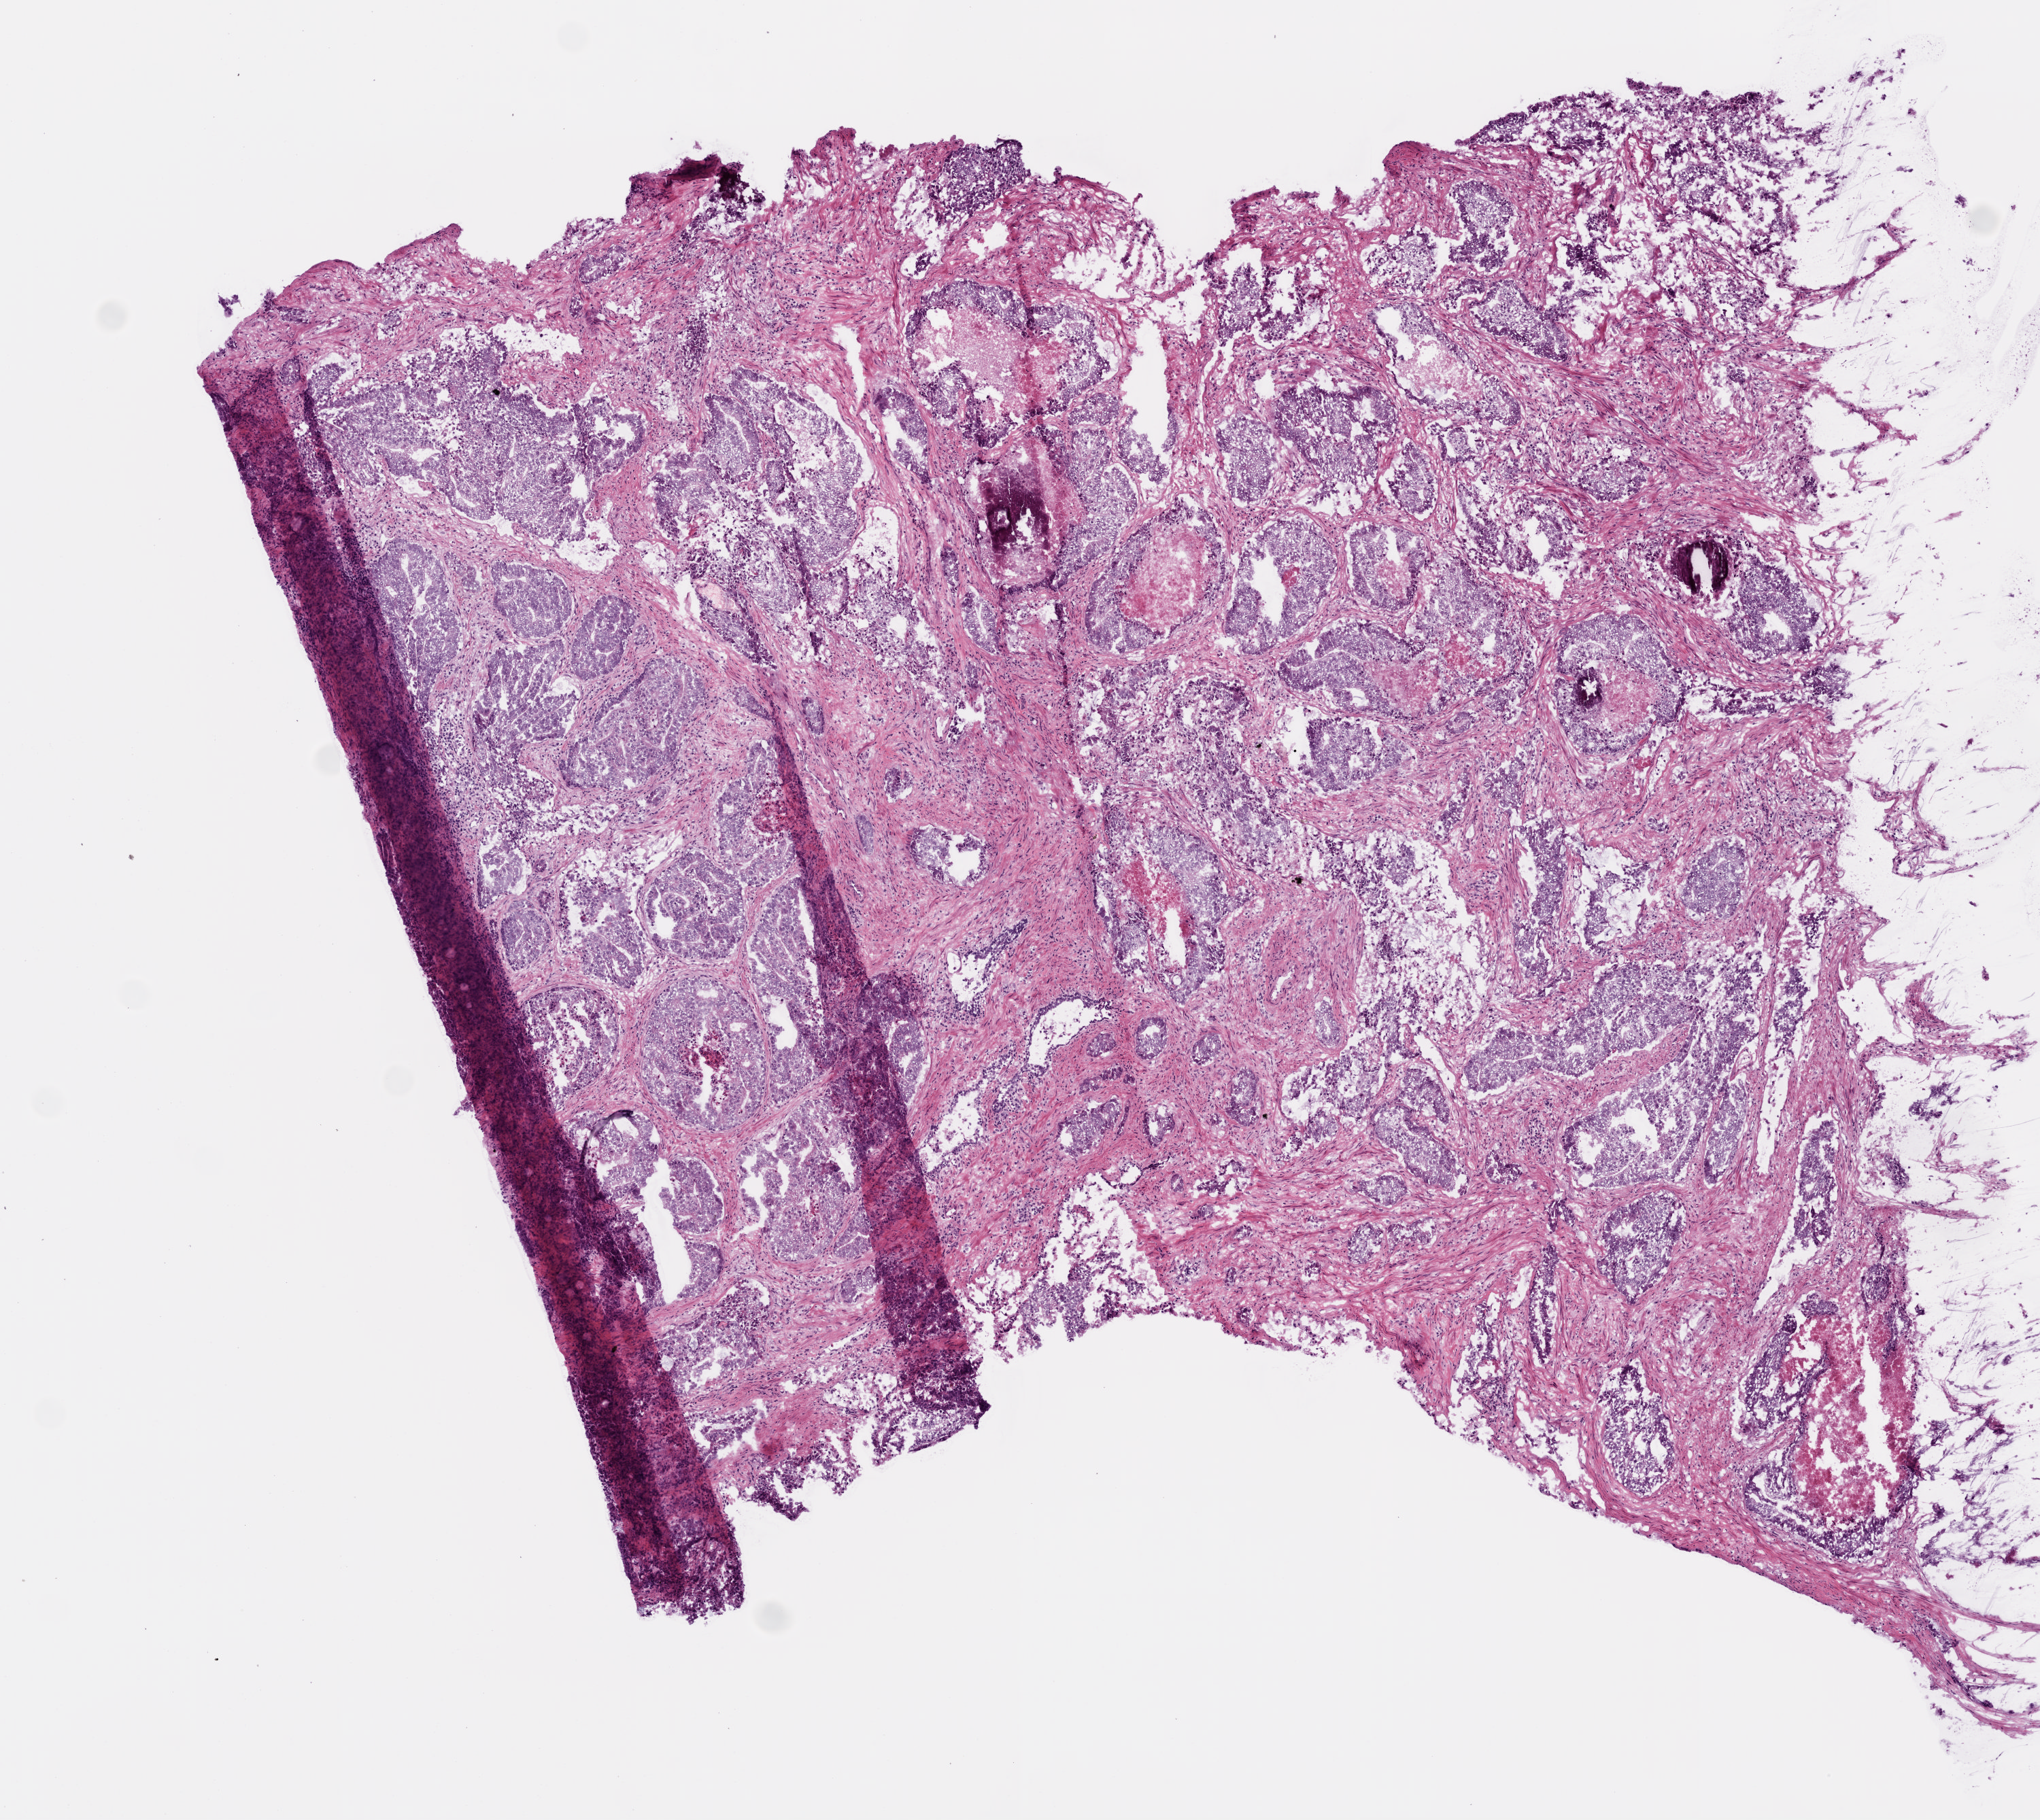
Digitized Hematoxylin and eosin (H&E) stained tissue section (whole slide) — whole scanned area (about 6.0 x 5.4 mm) shown as a low-resolution overview. Frozen section from the bottom of the tissue portion. Sample: primary tumour, prostate. Male, age 48 years at initial diagnosis. Gleason score: 9 (5+4). Slide review estimates, as recorded: tumour cells 40%, tumour nuclei 50%, normal cells 25%, stromal cells 20%, necrosis 15%. Infiltration values recorded for this section: lymphocyte infiltration 2%, monocyte infiltration 3%, neutrophil infiltration 0%.
Lymph nodes positive (case pathology): 0 of 8 examined. Diagnosis: Acinar cell carcinoma (prostate gland). Laterality: bilateral.